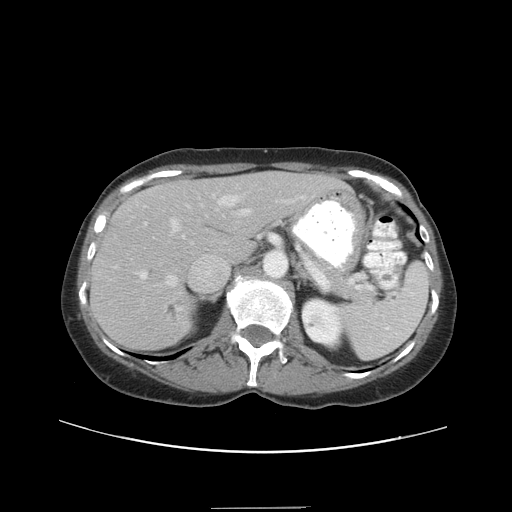
Contrast-enhanced abdominal CT, one axial slice; slice 25 of 38 in the series (ordered by position); reconstruction kernel STANDARD; 120 kVp; intravenous contrast given; soft-tissue window (W 400 / L 40 HU); 5 mm slice thickness; 512 × 512 image matrix, field of view 388 × 388 mm. Female patient, age 64 years. Case-level facts recorded for this patient, not image findings: diagnosis: colorectal cancer liver metastases, imaged before liver resection; multiple liver metastases: no; largest metastasis: 3.8 cm; chemotherapy before resection: yes.
Annotated regions visible in this slice (manually delineated by an expert):
- hepatic veins: bounding box <155,195,237,293> (left, top, right, bottom; pixels)
- liver: <92,172,336,348>
- planned liver remnant (the part of the liver to remain after resection): <136,172,336,262>
- portal vein (with intrahepatic branches): <137,201,287,279>